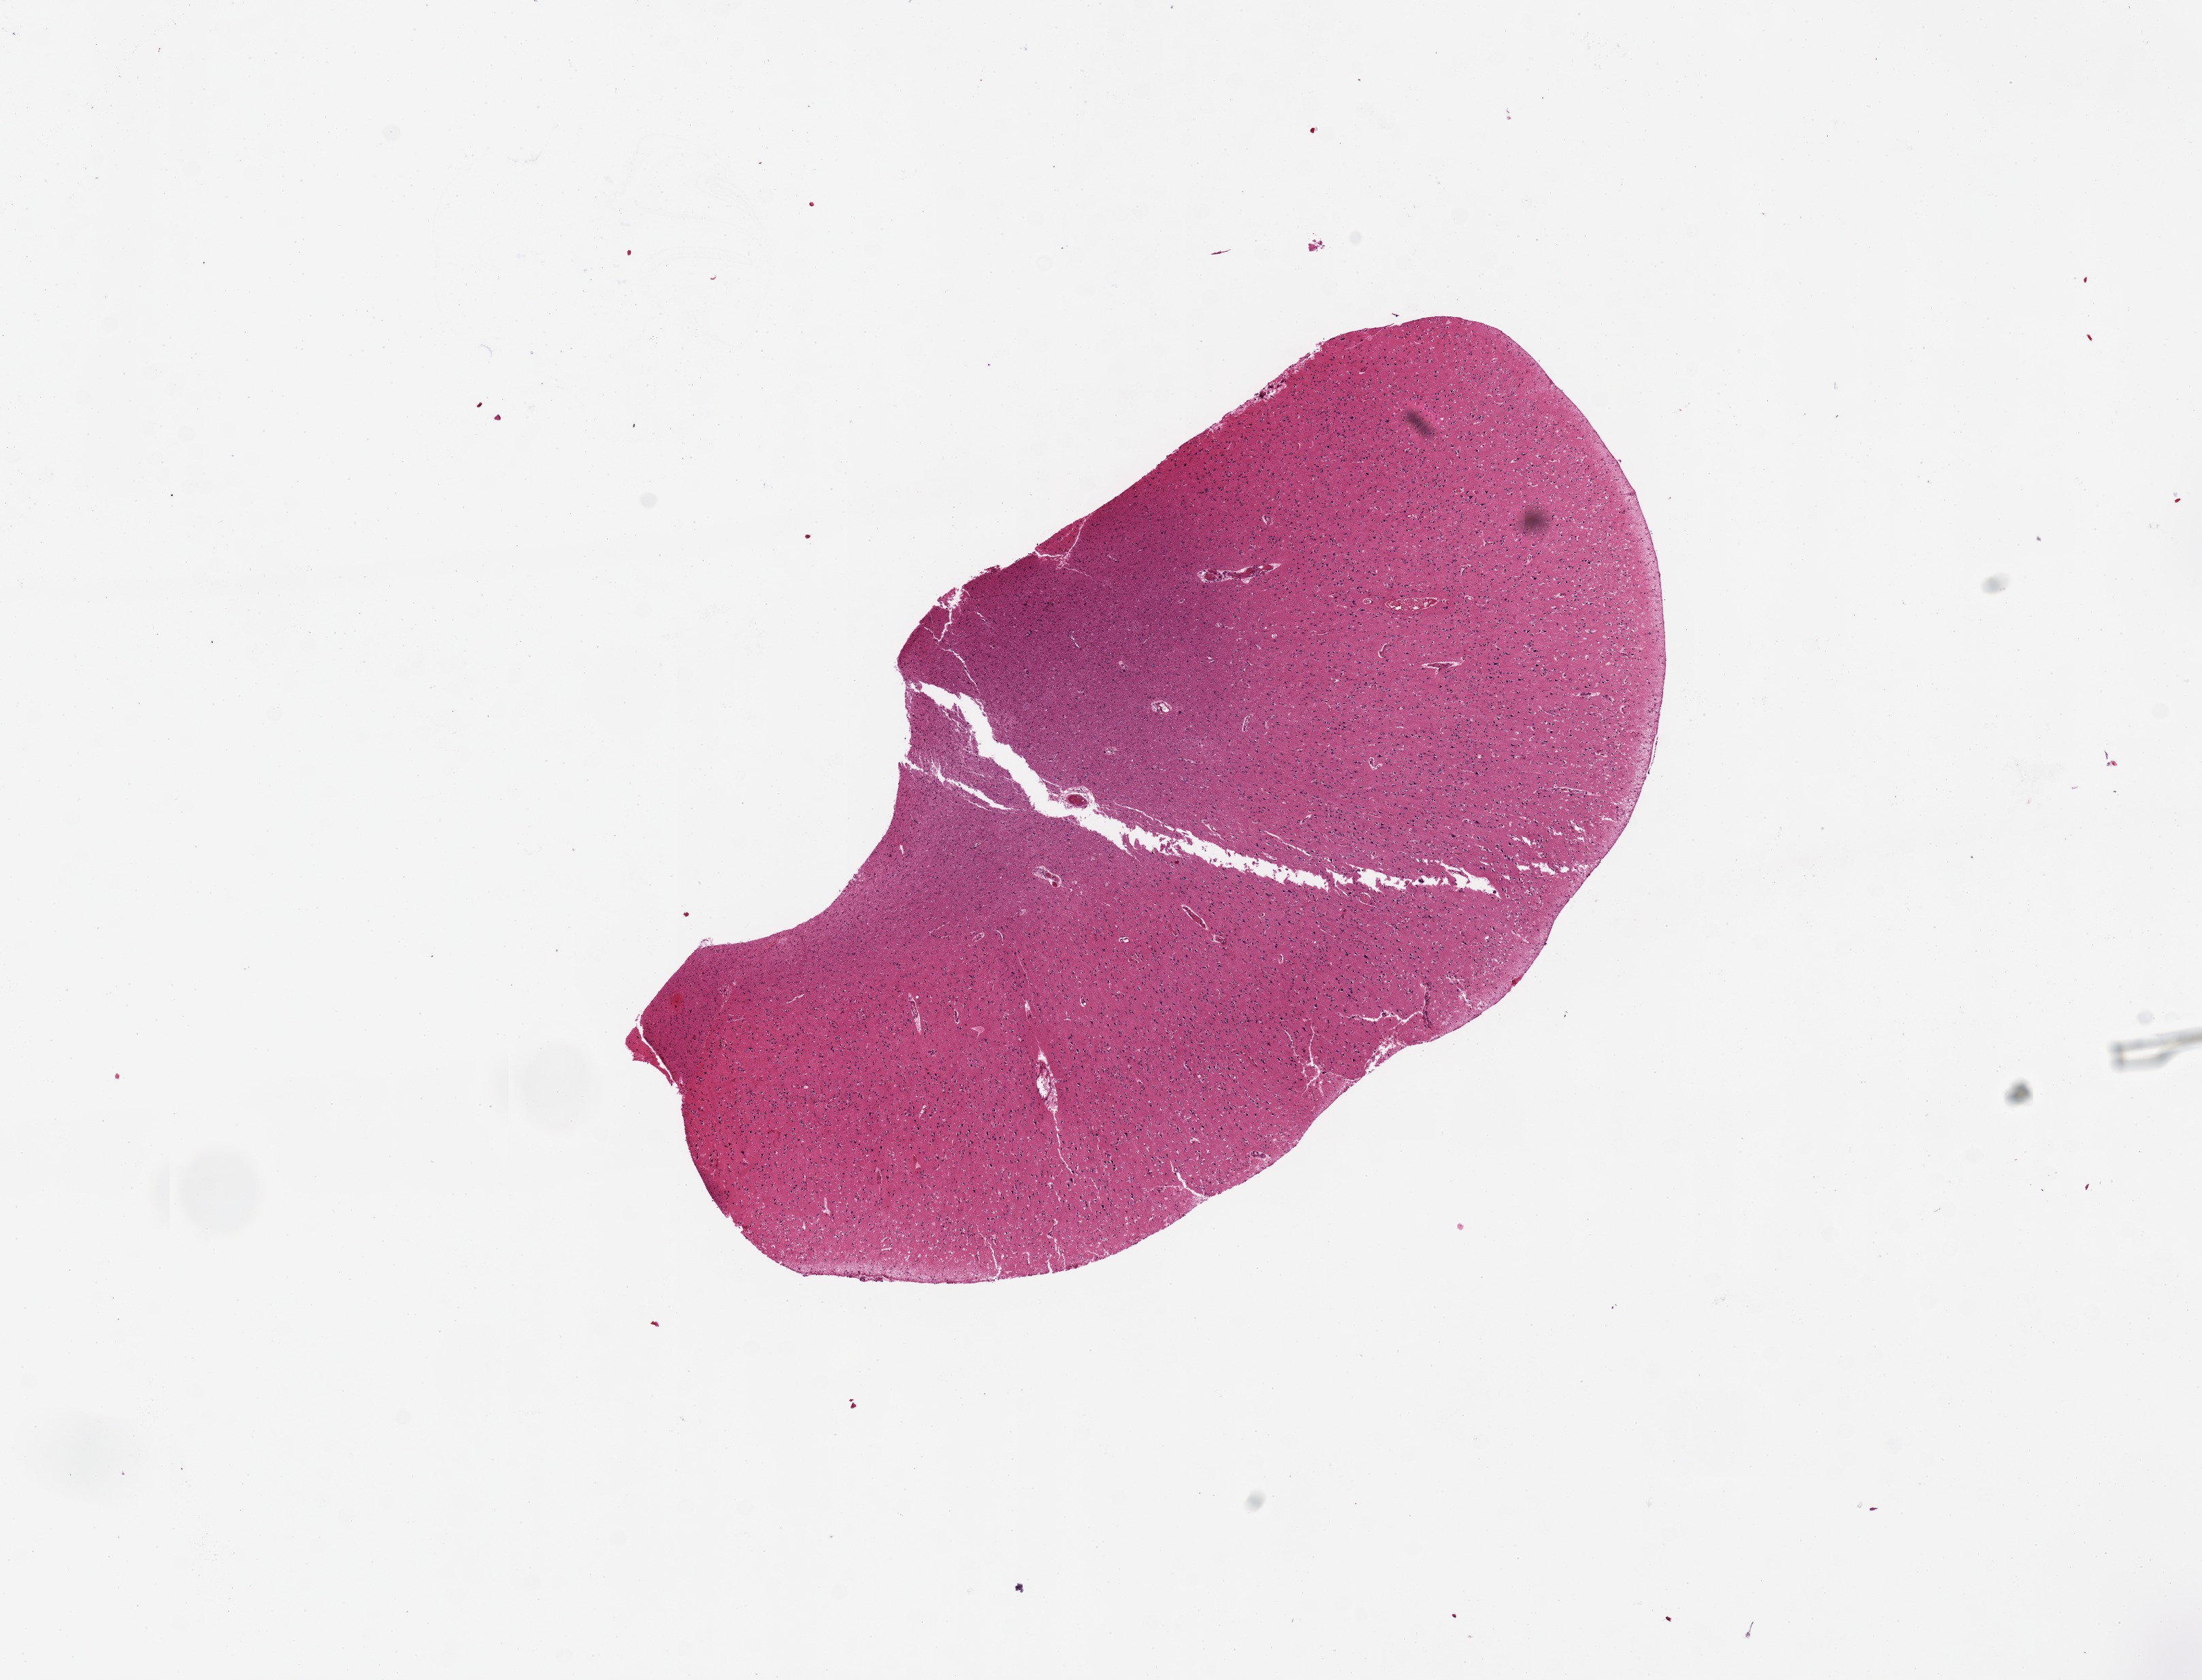
H&E whole-slide image — low-resolution overview of the scanned area, about 12.8 x 9.8 mm. PAXgene-fixed, paraffin-embedded tissue. Section of cerebral cortex (target tissue). Tissue donor sample. Female donor.
Pathologist's review note for this sample: 1, 6.6x3.6 mm.